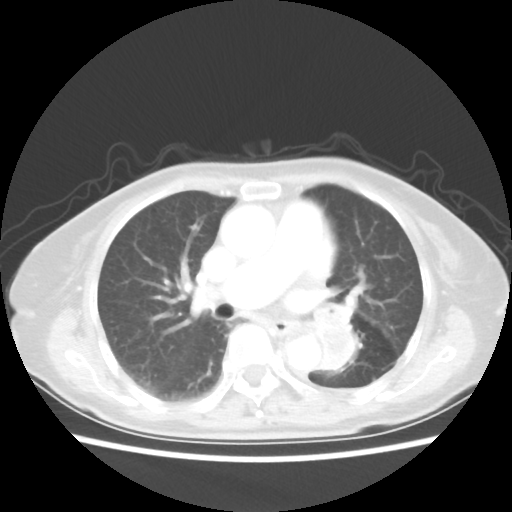
Chest CT, one axial slice. Position 28 of 50 along the scan axis. Reconstruction kernel STANDARD. 80 kVp. Lung window (W 1500 / L -600 HU). 512 × 512 image matrix. Patient: female, 81 years. From the clinical record (not read from this slice): clinical TNM (as recorded): T2 N0 M1a.
Structures marked on this image (rectangle marked by the reading radiologist):
- lung tumour (recorded histology: squamous cell carcinoma): box from (x=309, y=312) to (x=363, y=377) px